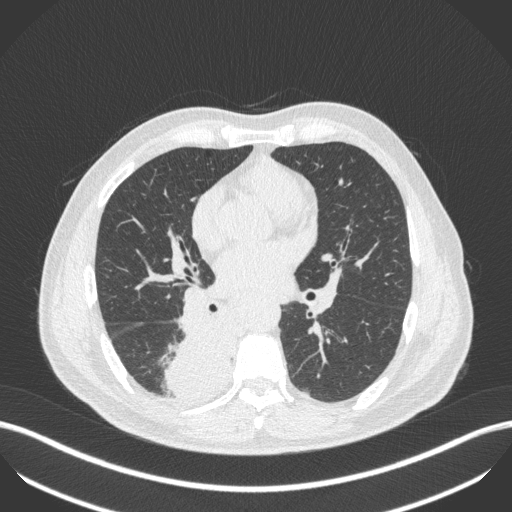
Chest CT, one axial slice. Slice 238 of 451 in the series (ordered by position). Lung window (W 1500 / L -600 HU). 1 mm slice thickness. 512 × 512 image matrix, field of view 400 × 400 mm. Patient: male, 61 years. Case-level facts recorded for this patient, not image findings: clinical TNM (as recorded): T1 N0 M0; histopathological grade: G3.
Annotated regions visible in this slice (bounding box drawn by a radiologist):
- lung tumour (recorded histology: small cell carcinoma): bounding box <162,311,242,414> (left, top, right, bottom; pixels)